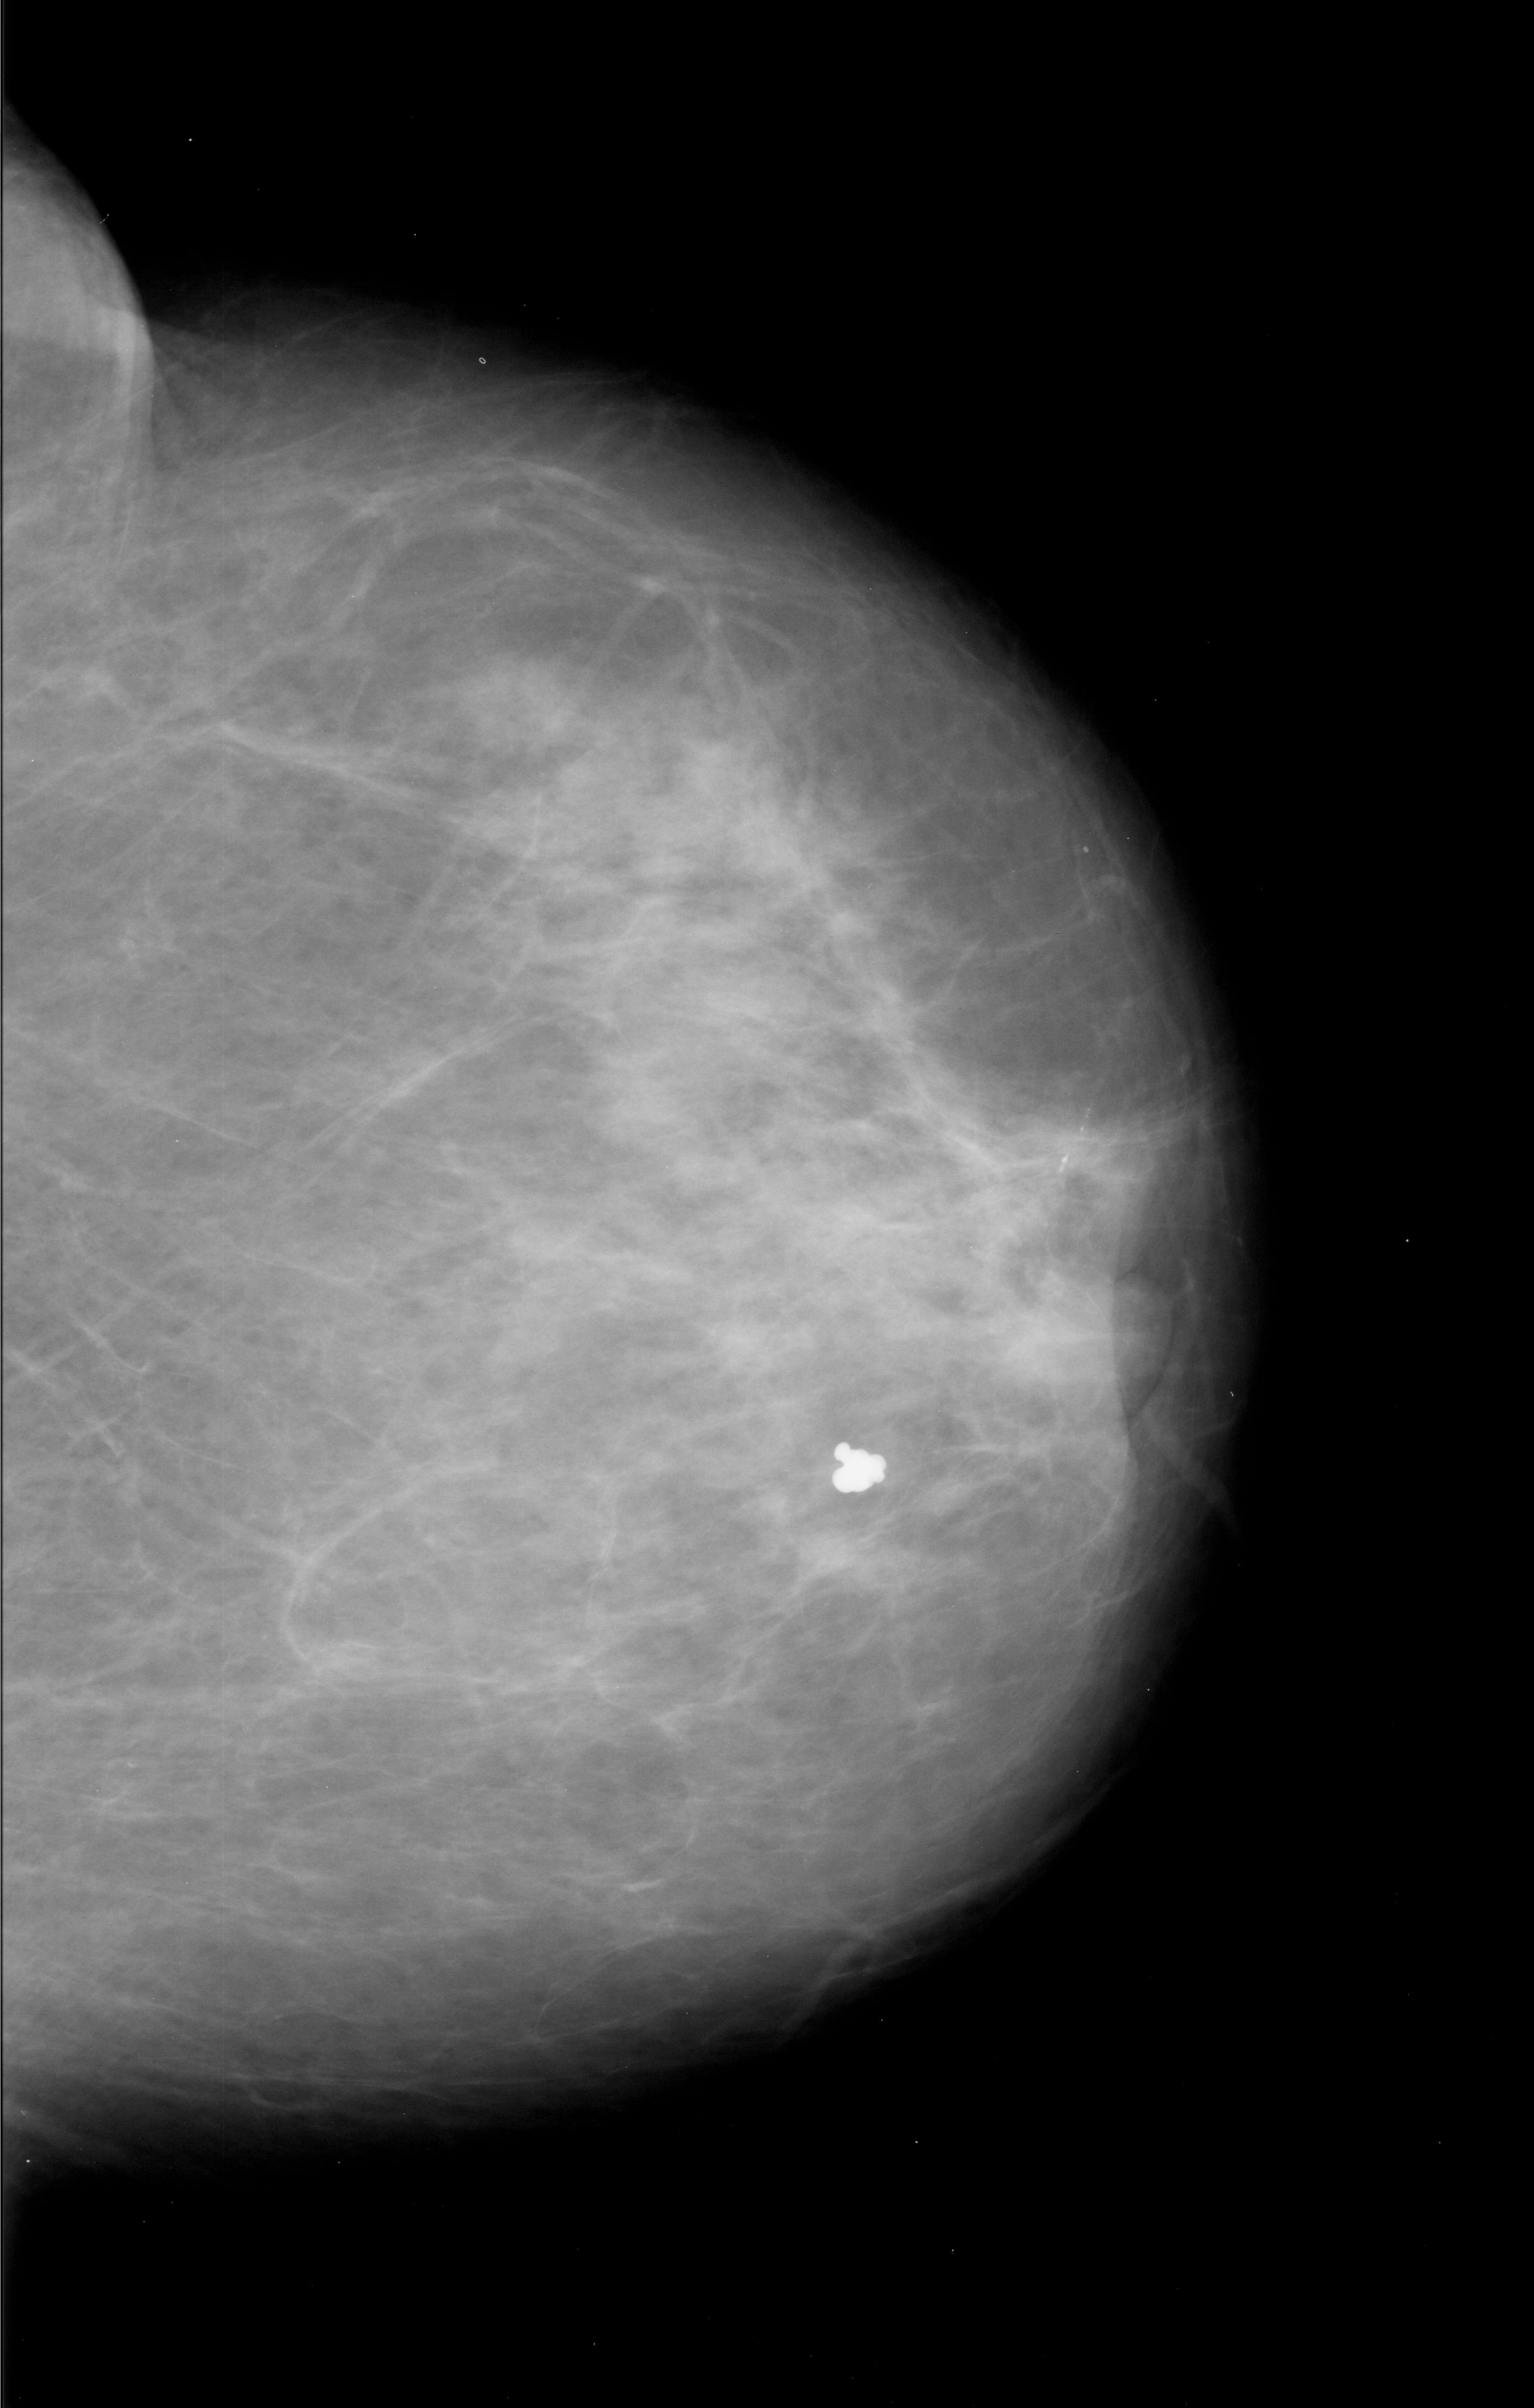
Mammogram (digitized film), right breast, craniocaudal (CC) view, BI-RADS breast density category 3 (scale 1–4).
Calcifications, morphology pleomorphic, distribution linear; BI-RADS assessment category 4; pathology result (as recorded, not read from the image): malignant.